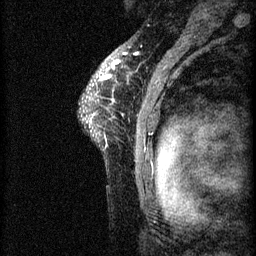
Breast MRI (dynamic contrast-enhanced), one sagittal slice; slice 51 of 60 in the series (ordered by position); 3 images stored at this slice position (order not interpretable as contrast timing); 1.5 T; TE 4.2 ms, TR 8.2 ms; 2 mm slice thickness; 256 × 256 image matrix, field of view 180 × 180 mm. Patient: female, 41 years.
Annotated regions visible in this slice (semi-automatically segmented with operator editing):
- analysis volume of interest (the breast-tissue region the enhancement analysis was run in; not a lesion): bounding box [x1, y1, x2, y2] px = [80, 62, 160, 175]
- tumour enhancement mask (voxels above the 70 % enhancement threshold inside the analysis volume of interest): [99, 62, 120, 81]